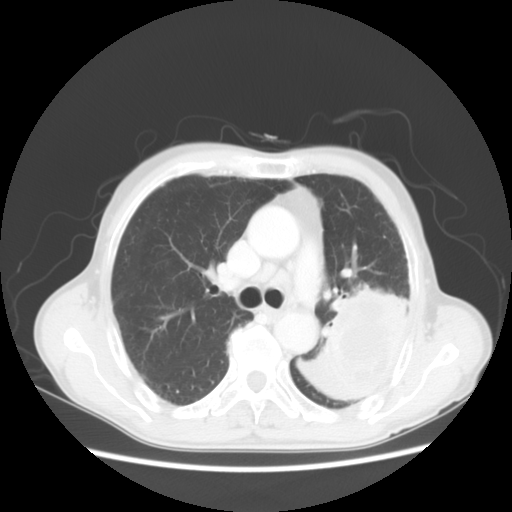
Chest CT, one axial slice. Position 33 of 51 along the scan axis. 120 kVp. Lung window (W 1500 / L -600 HU). 512 × 512 image matrix, field of view 360 × 360 mm. Male patient, age 64 years. Case-level facts recorded for this patient, not image findings: clinical TNM (as recorded): T4 N0 M0.
Annotated regions visible in this slice (rectangle marked by the reading radiologist):
- lung tumour (recorded histology: squamous cell carcinoma): bounding box [x1, y1, x2, y2] px = [311, 286, 410, 420]